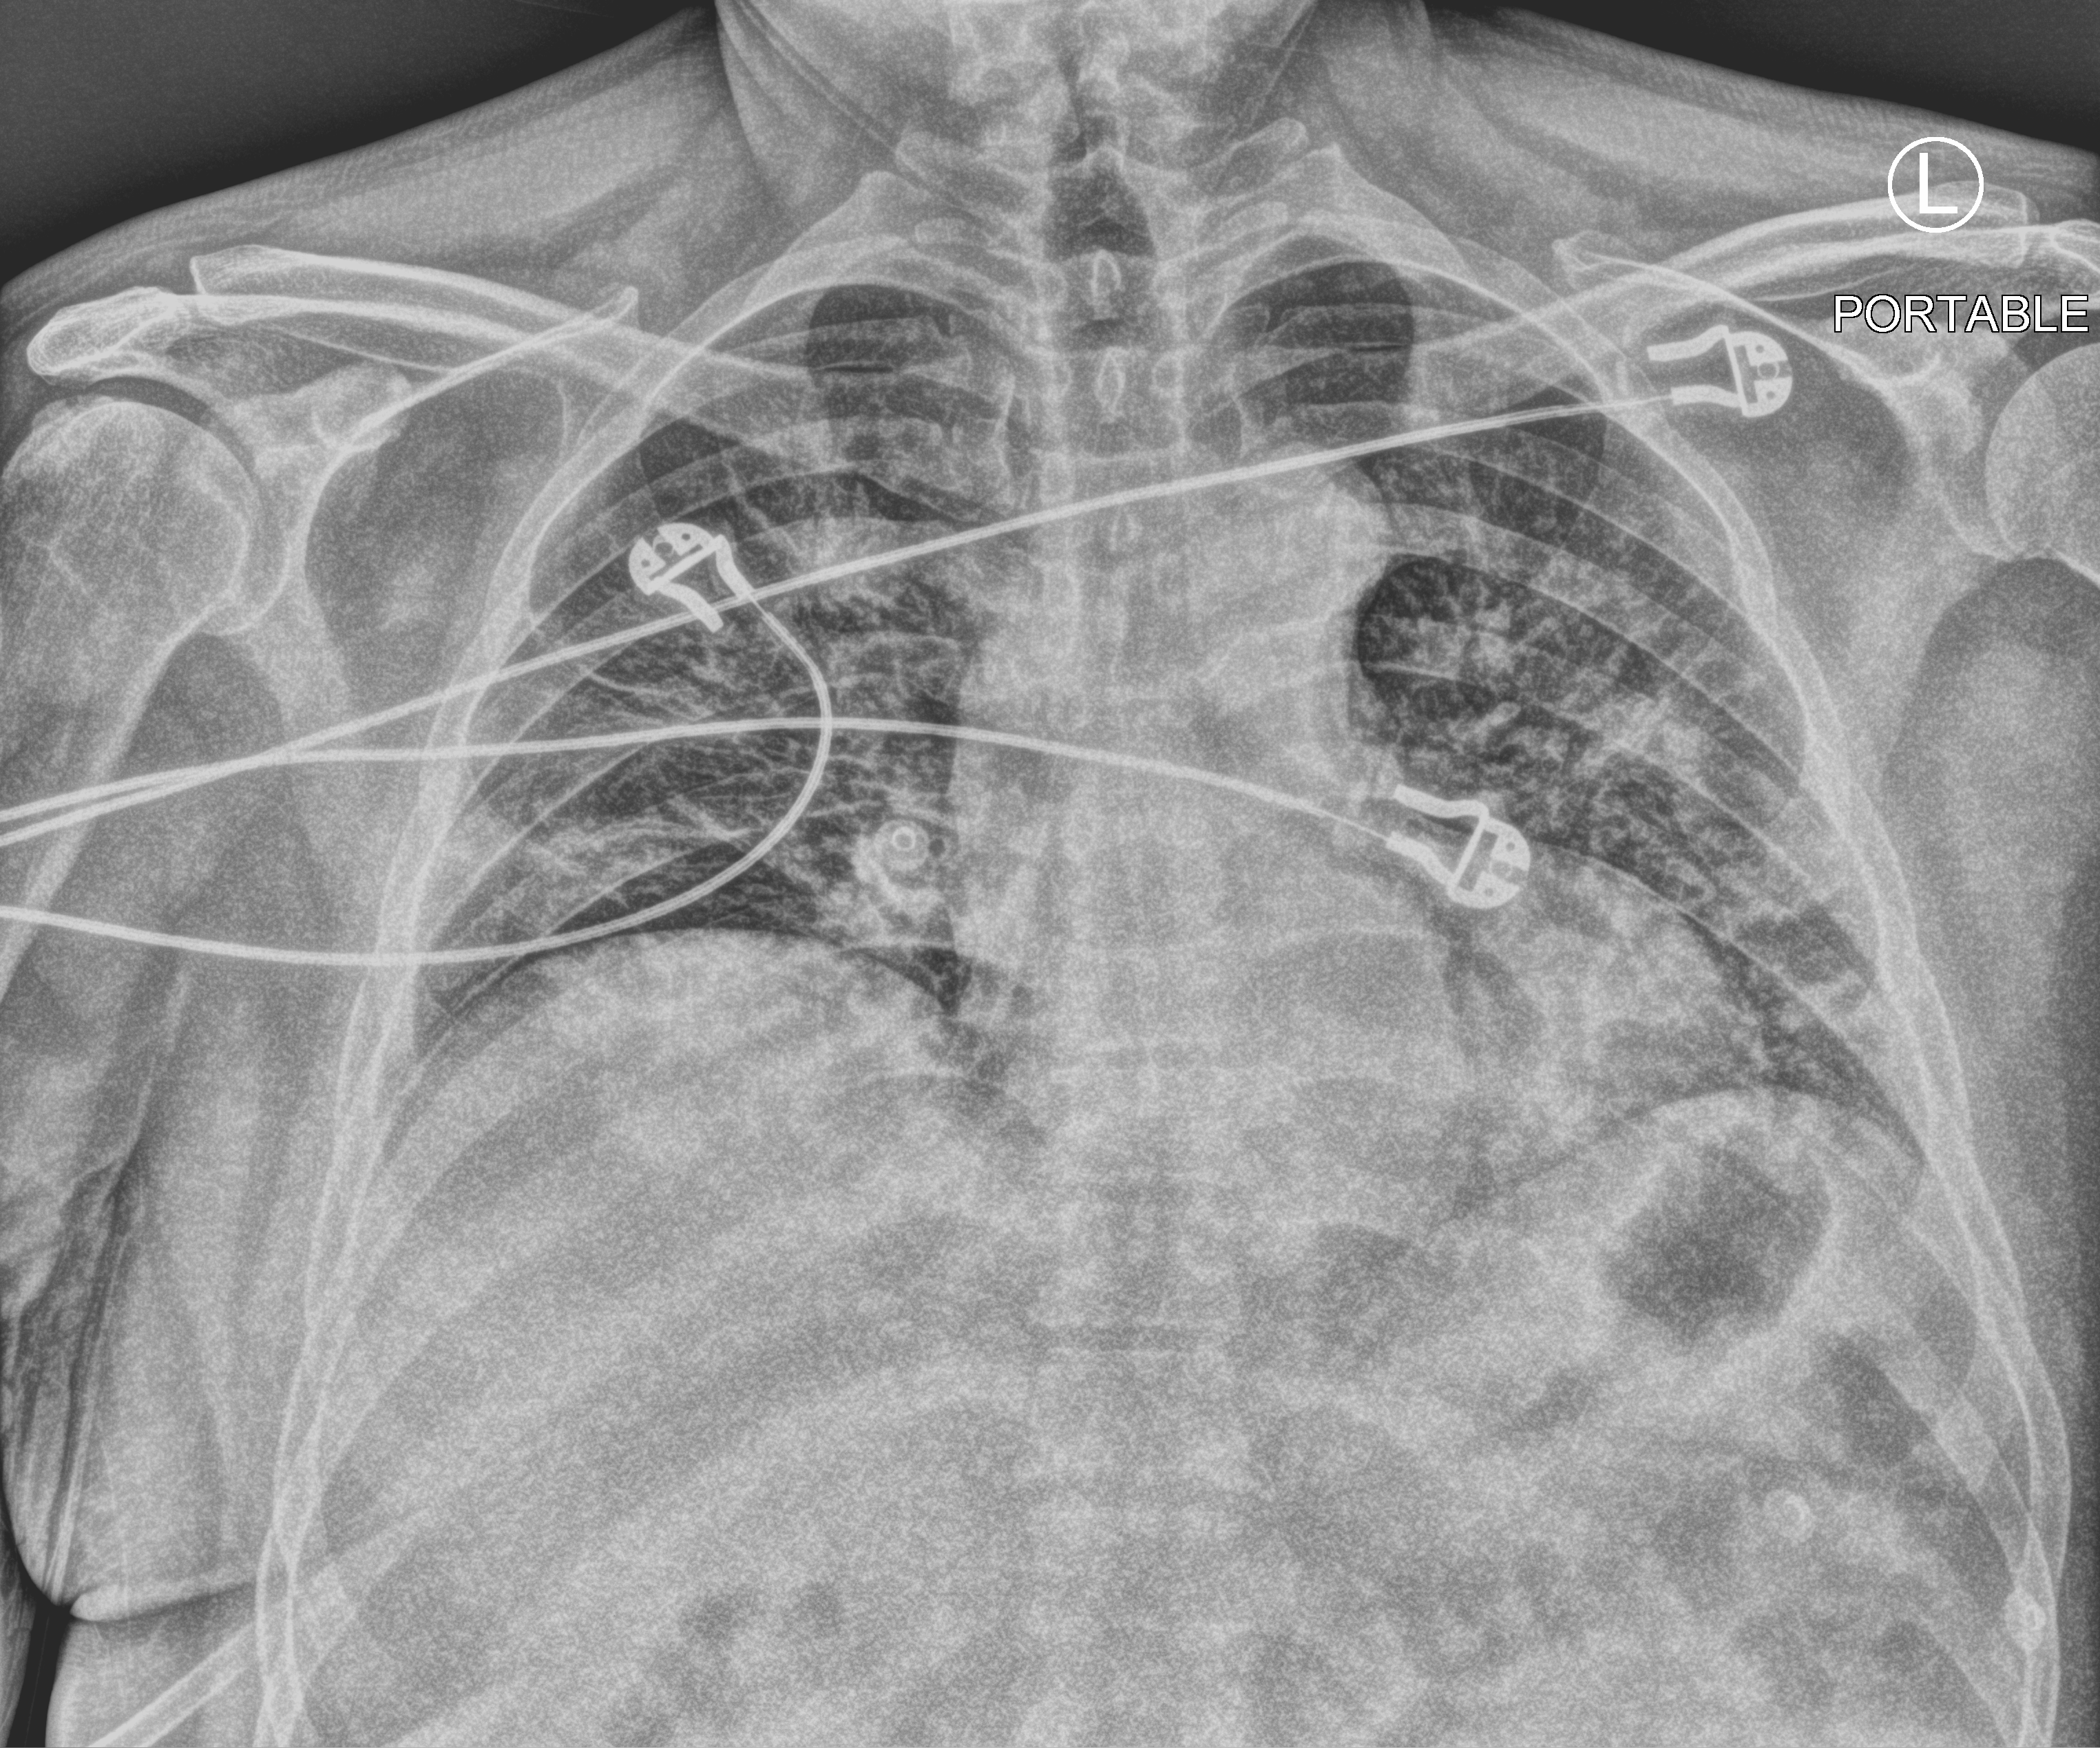
Chest X-ray (portable); anteroposterior (AP) projection. Patient hospitalised with COVID-19; male, aged 18–59 years.
Admission-level facts for this patient (not findings on this image; timing relative to this image not recorded): mechanically ventilated during this hospital stay: no; admitted to intensive care during this hospital stay: no; diabetes (admission record): yes.